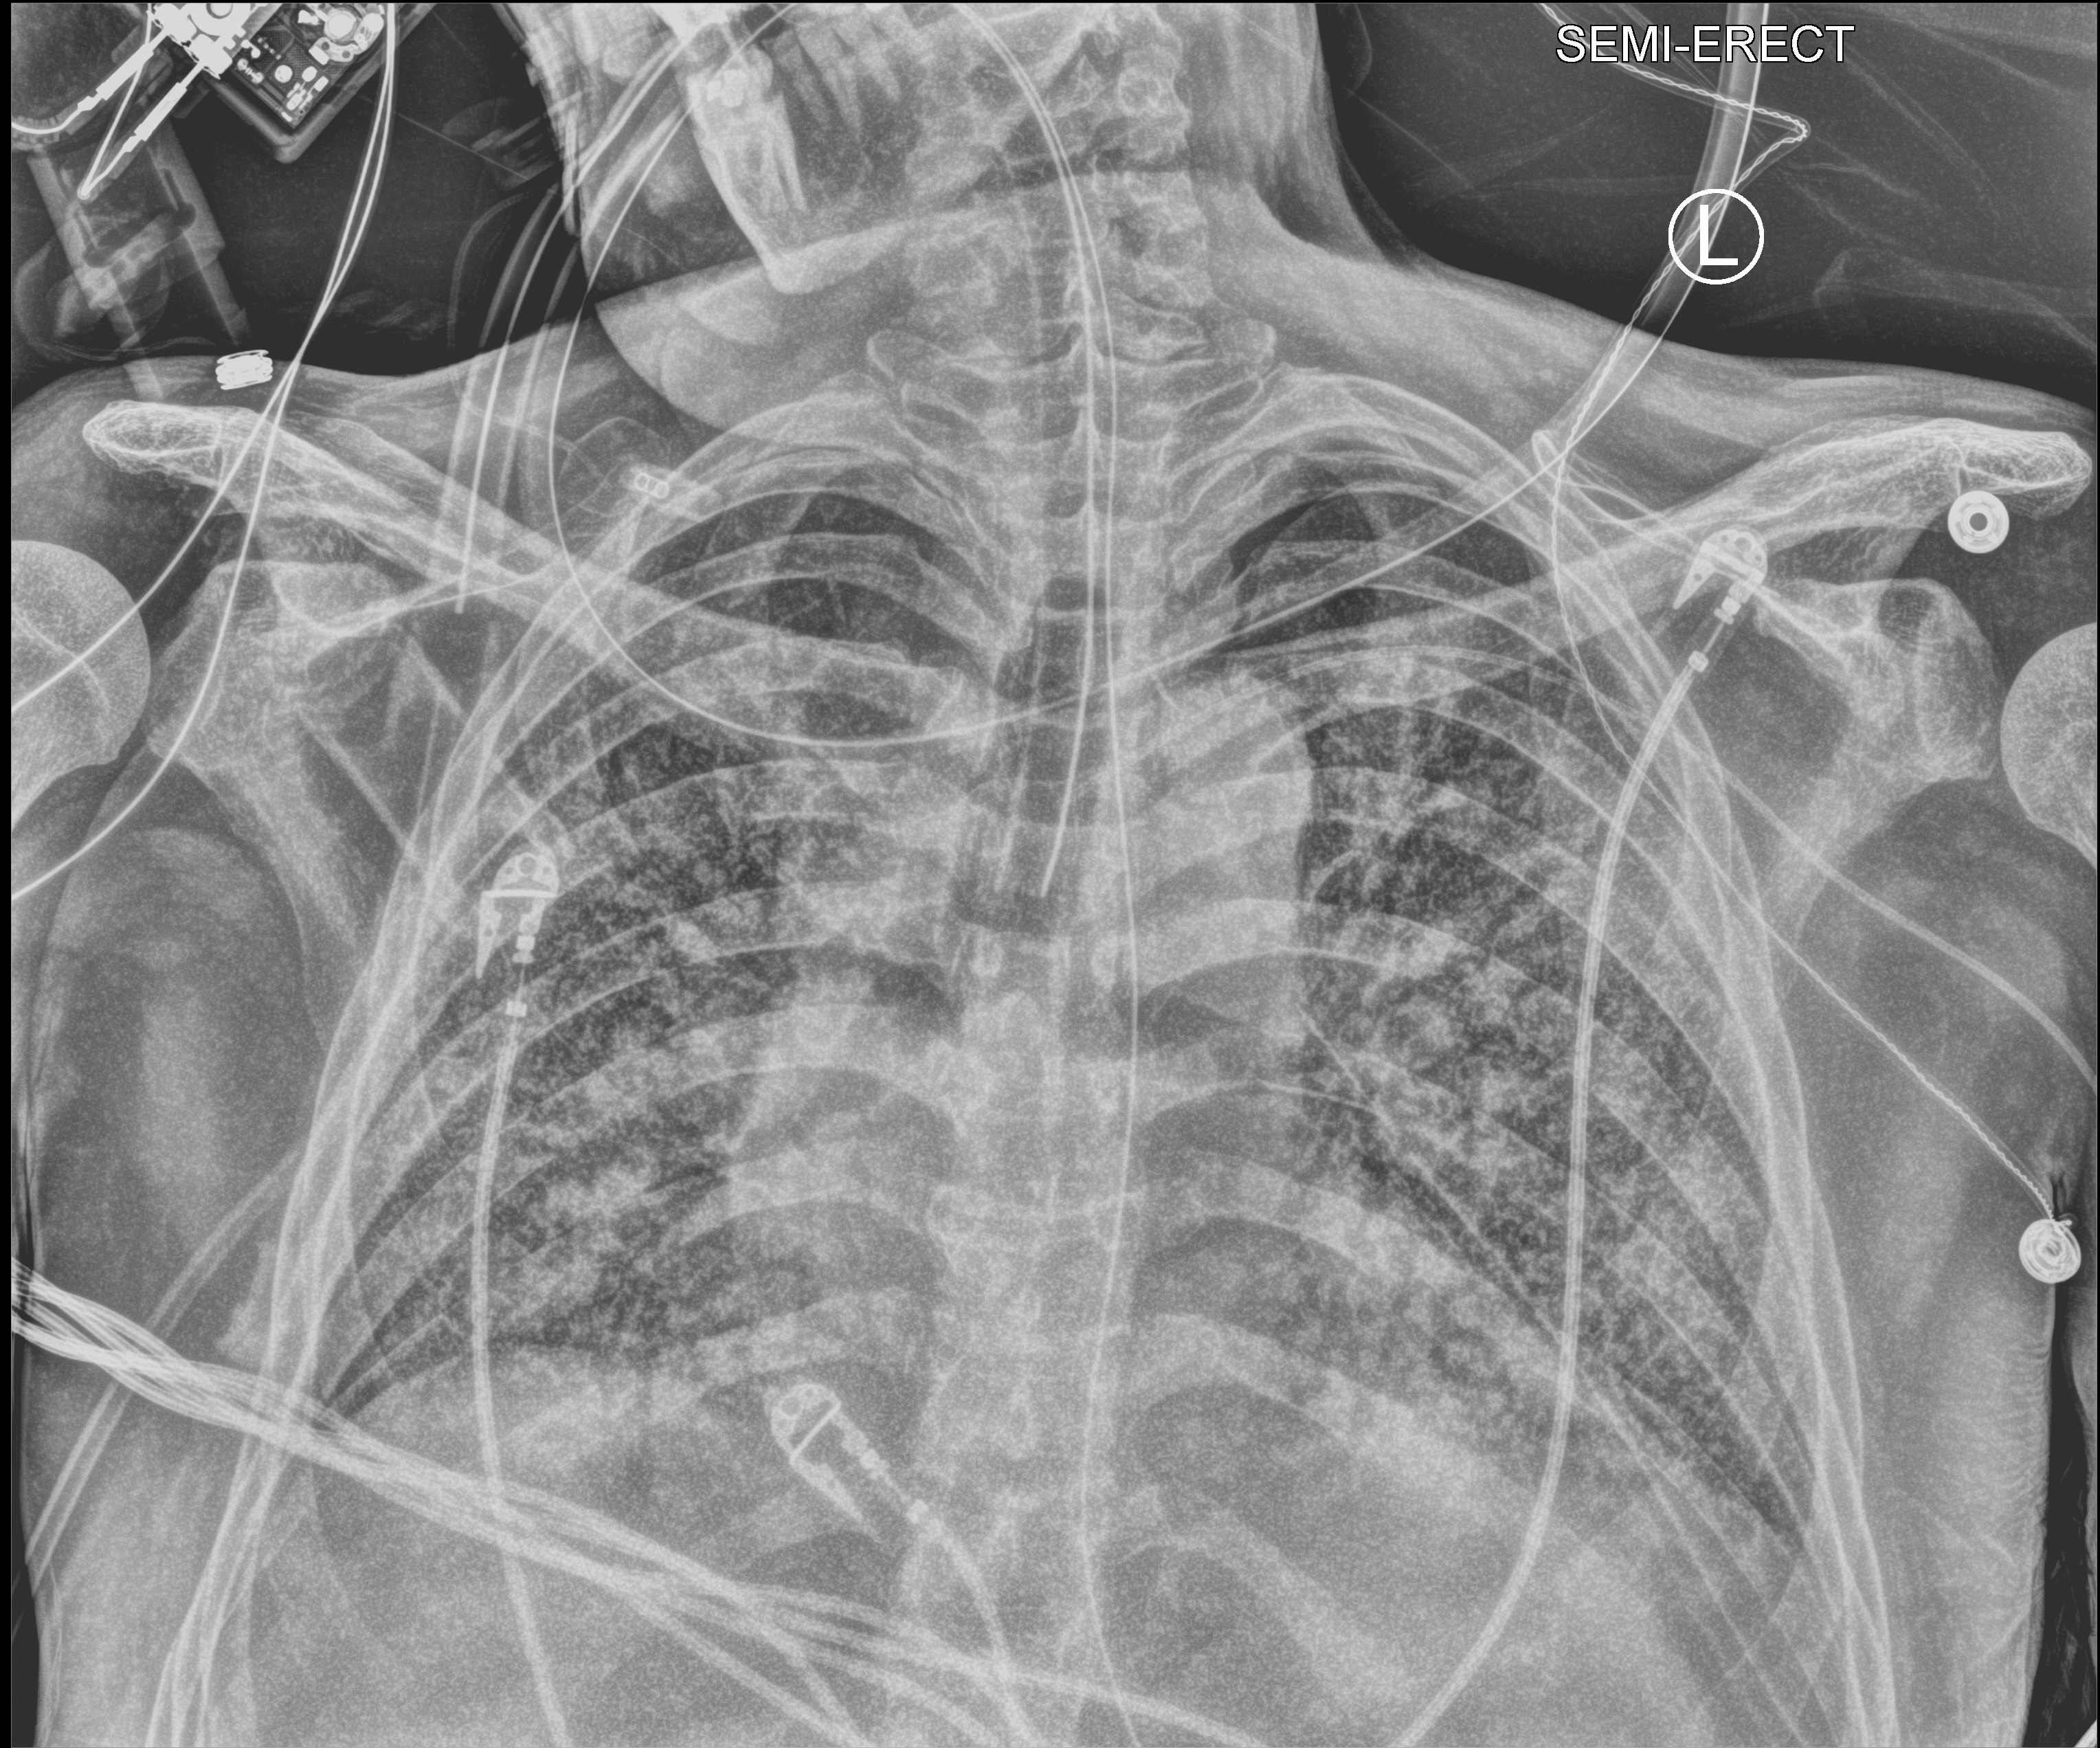
Portable chest radiograph, anteroposterior (AP) projection. Patient hospitalised with COVID-19; male, aged 60–74 years.
Hospital-stay facts (about this admission, not read from this image; timing relative to this image not recorded): length of hospital stay: 54 days.